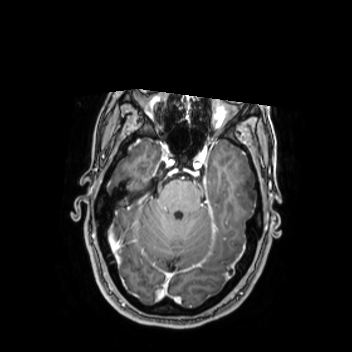
Brain MRI from a brain-tumour surgery series, one axial slice. Slice 174 of 350 in the series (ordered by position). T1-weighted post-contrast. 352 × 352 image matrix. From the clinical record (not read from this slice): histopathology: Oligodendroglioma; WHO grade: 2.
Structures marked on this image (manually delineated by an expert):
- tumour: bounding box (x1, y1, x2, y2) in pixels: (224, 169, 262, 201)